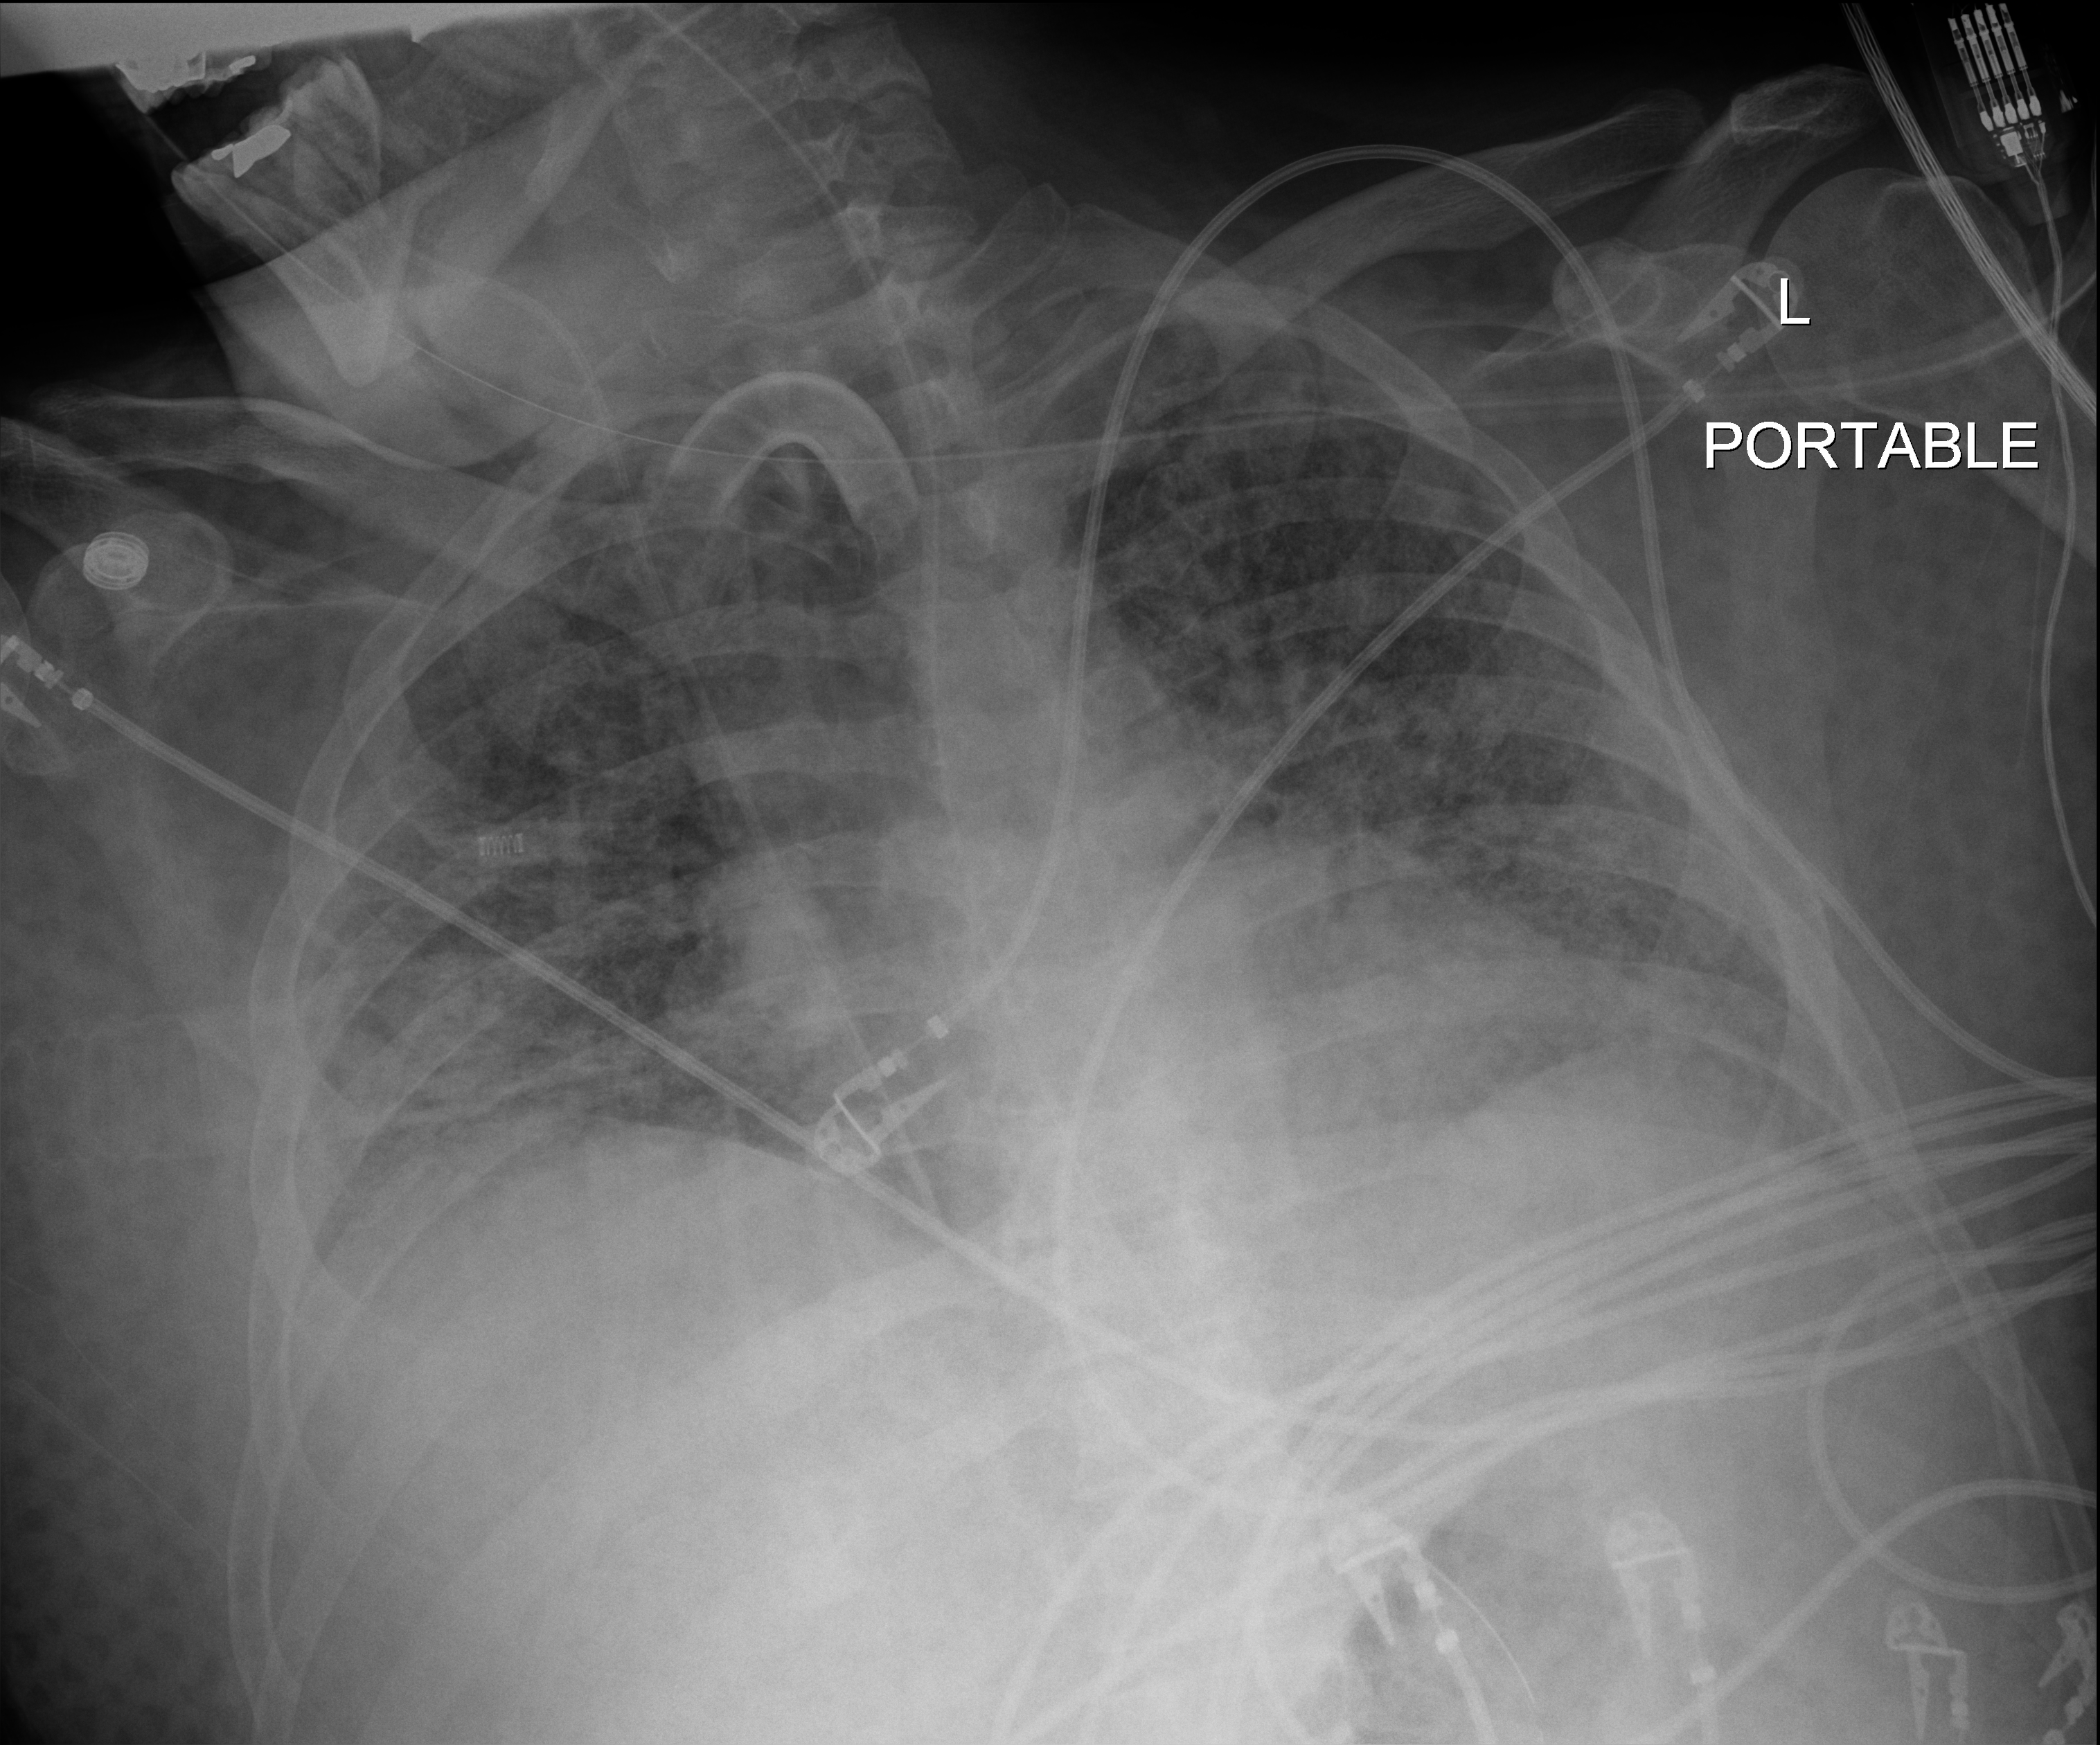
Chest X-ray (portable); anteroposterior (AP) projection. Male patient hospitalised with COVID-19, age 18–59 years.
Admission-level facts for this patient (not findings on this image; timing relative to this image not recorded):
- mechanically ventilated during this hospital stay: yes
- admitted to intensive care during this hospital stay: yes